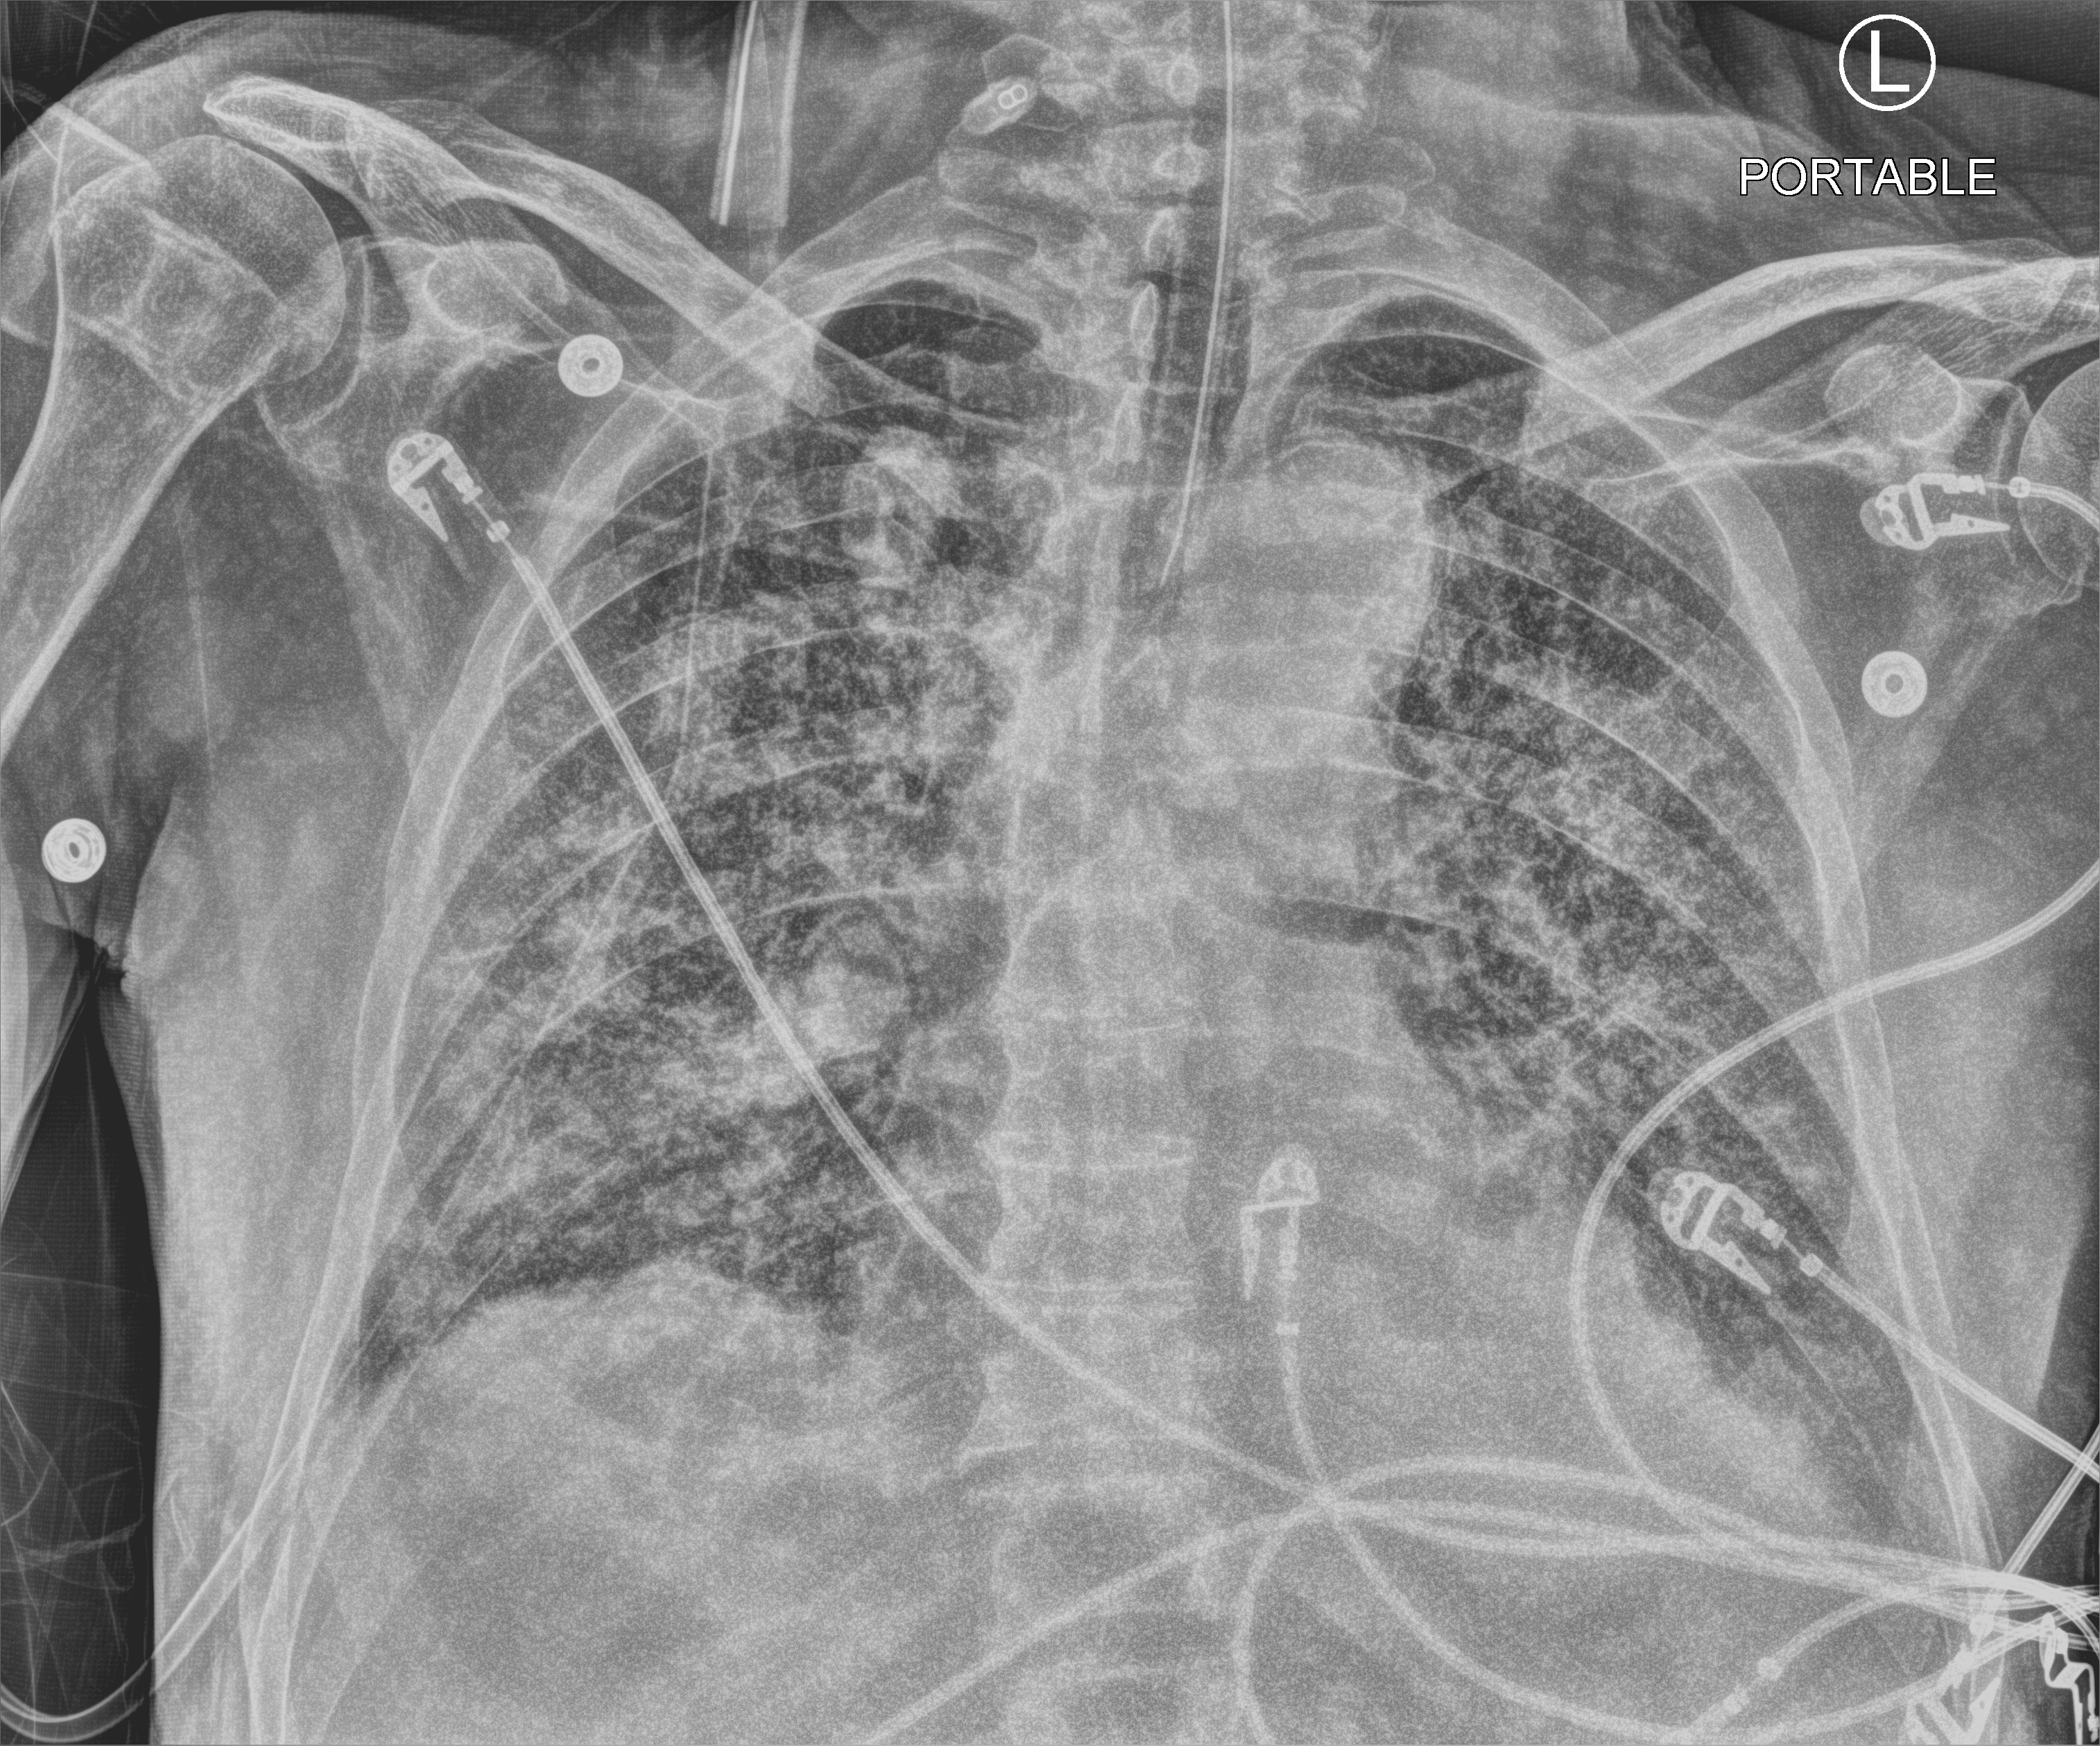
Chest X-ray (portable). Patient hospitalised with COVID-19; male, aged 75–90 years.
From the hospital-stay record, not from the radiograph (when in the stay this image was taken is not recorded):
- mechanically ventilated during this hospital stay: yes
- admitted to intensive care during this hospital stay: yes